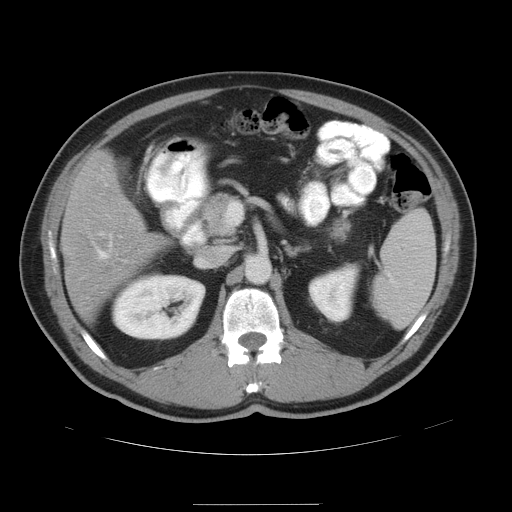
Contrast-enhanced abdominal CT, one axial slice. Slice 24 of 47 in the series (ordered by position). Intravenous contrast given. Soft-tissue window (W 400 / L 40 HU). 5 mm slice thickness. 512 × 512 image matrix, field of view 420 × 420 mm. Male patient, age 61 years. From the clinical record (not read from this slice): diagnosis: colorectal cancer liver metastases, imaged before liver resection; multiple liver metastases: no; largest metastasis: 1.2 cm; chemotherapy before resection: yes.
Outlined on this slice (manually delineated by an expert):
- hepatic veins: box from (x=99, y=250) to (x=108, y=258) px
- liver: (x=63, y=151)–(x=163, y=320)
- planned liver remnant (the part of the liver to remain after resection): (x=67, y=151)–(x=163, y=321)
- liver metastasis: (x=62, y=242)–(x=75, y=251)